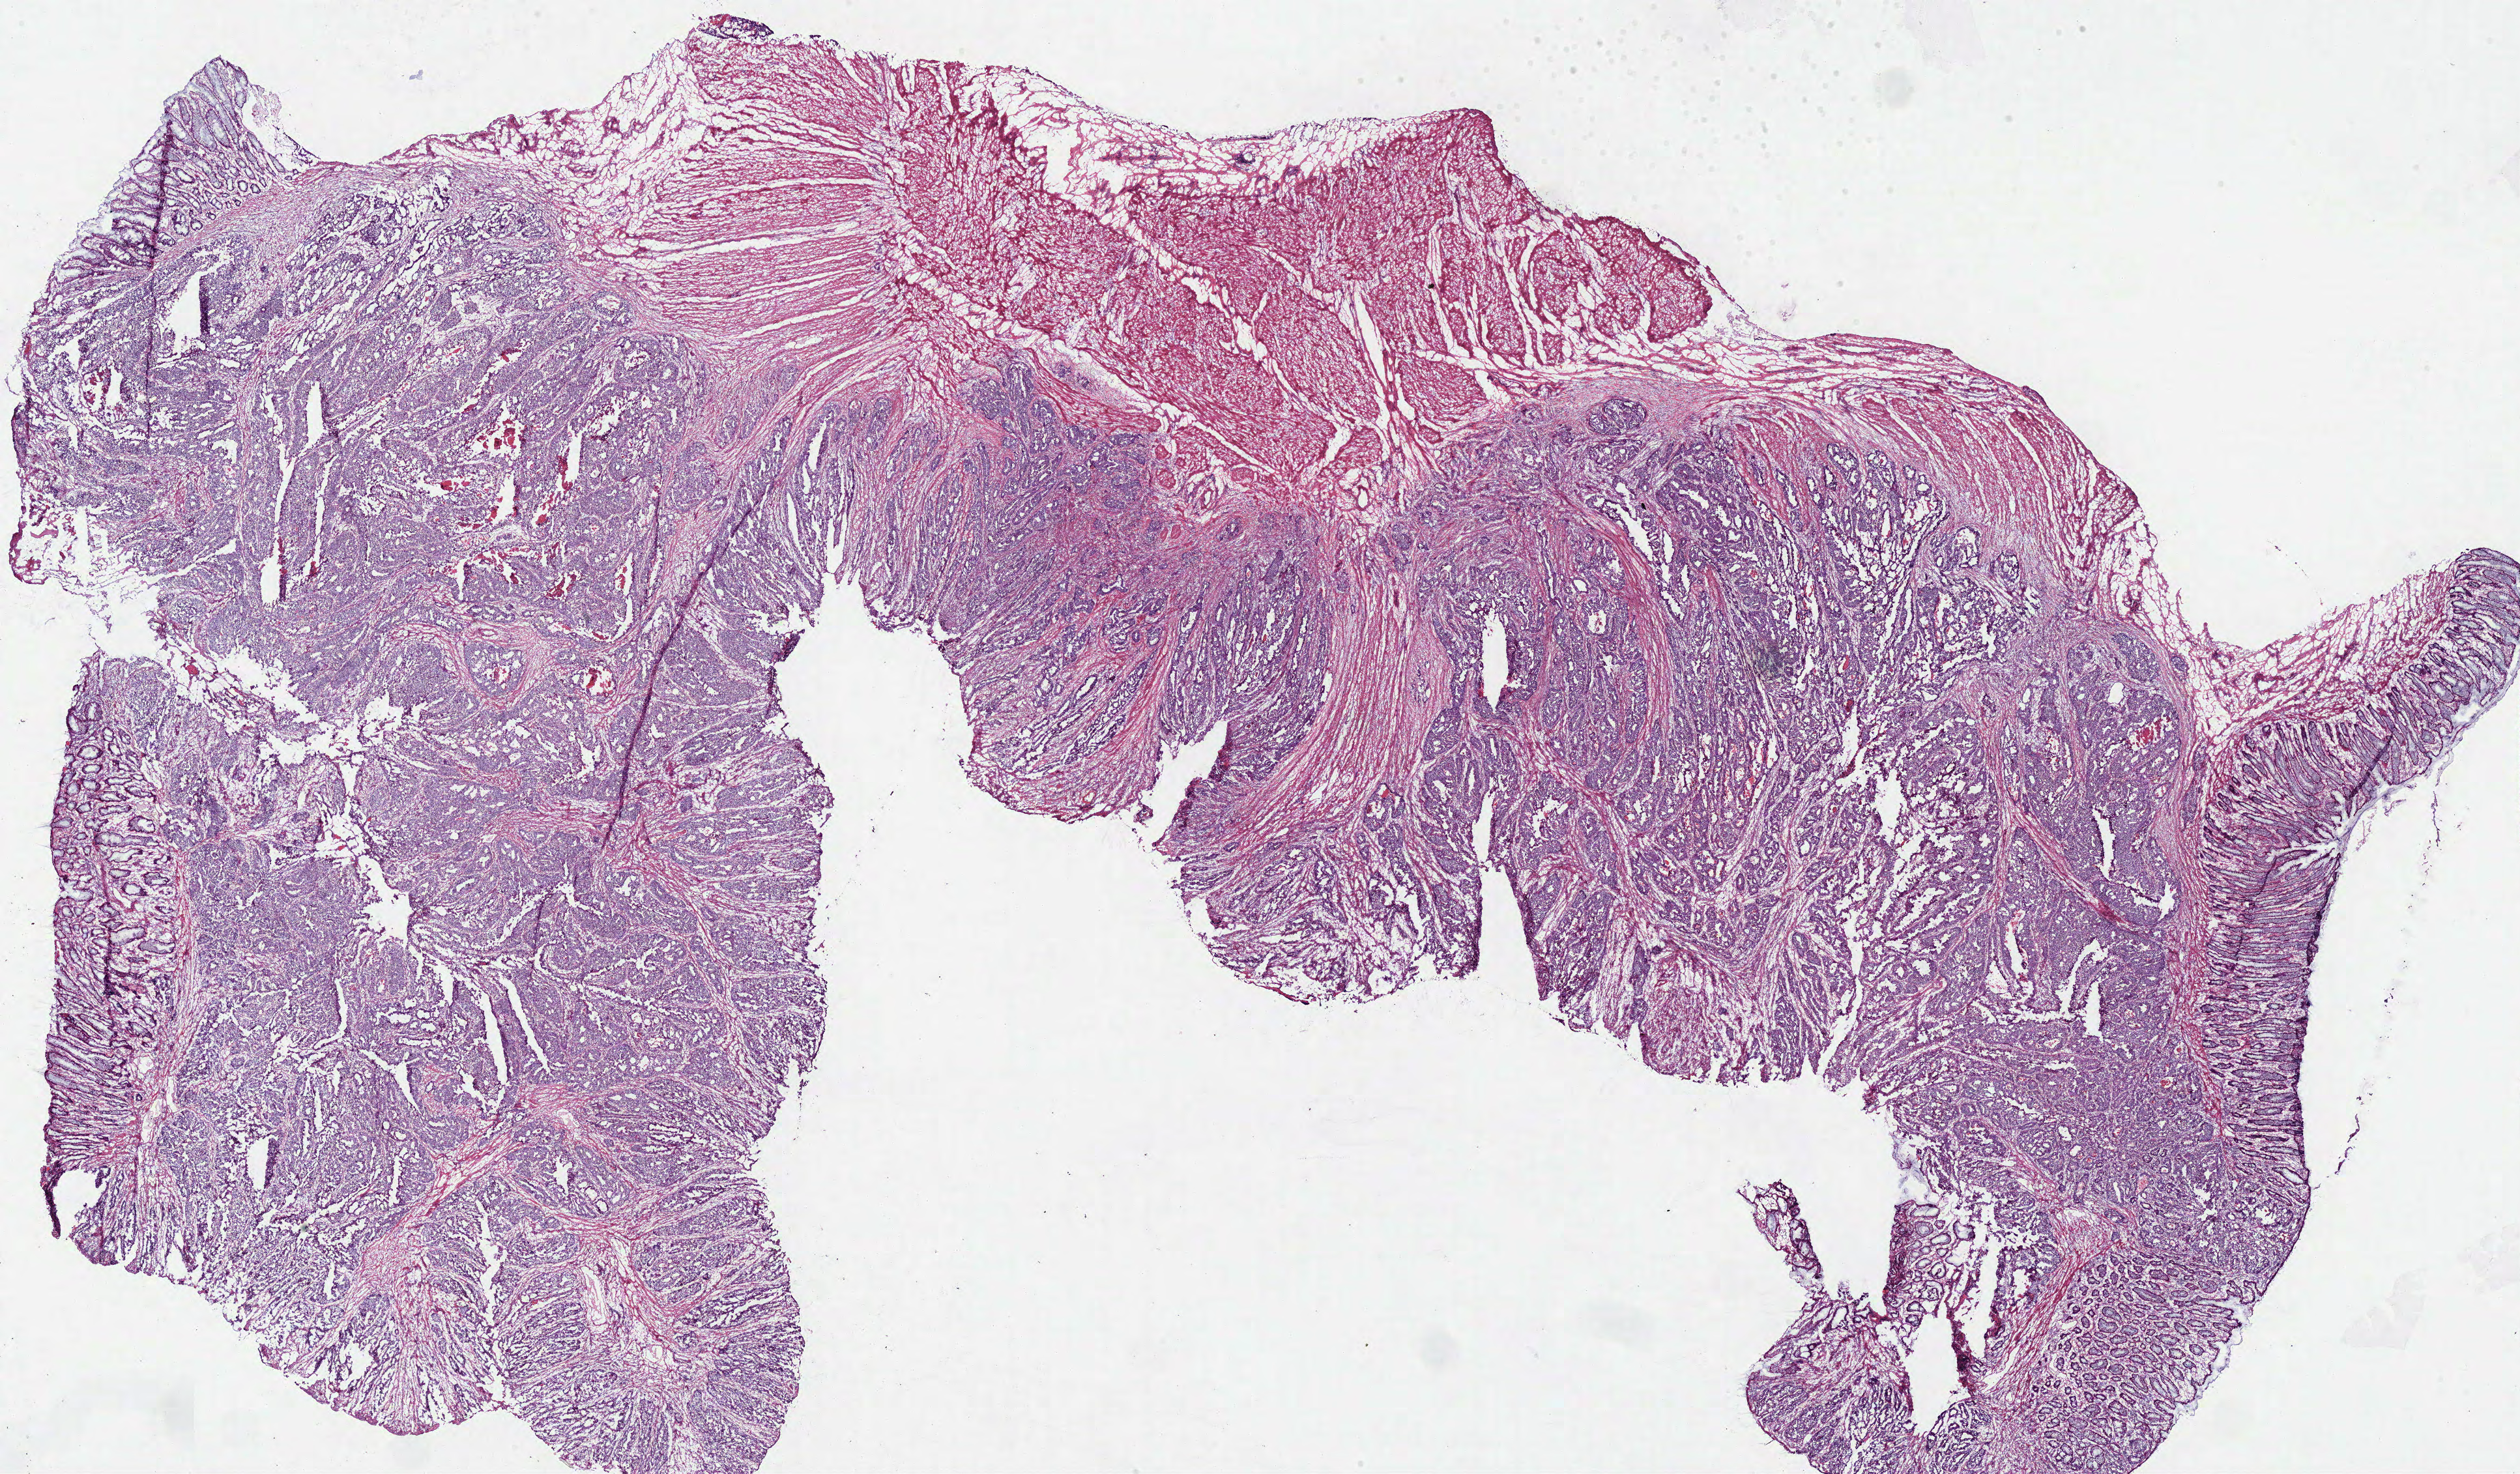
Digitized H&E-stained tissue section (whole slide), shown as a low-resolution overview of the whole scanned area (about 30.5 x 17.8 mm, slide scanned at 40x). Composition of this section per pathologist review: tumour cells 75%, tumour nuclei 80%, normal cells 20%, necrosis 5%. Infiltration values recorded for this section: lymphocyte infiltration 10%, neutrophil infiltration 2%.
• specimen: frozen section; rectum, primary tumour sample